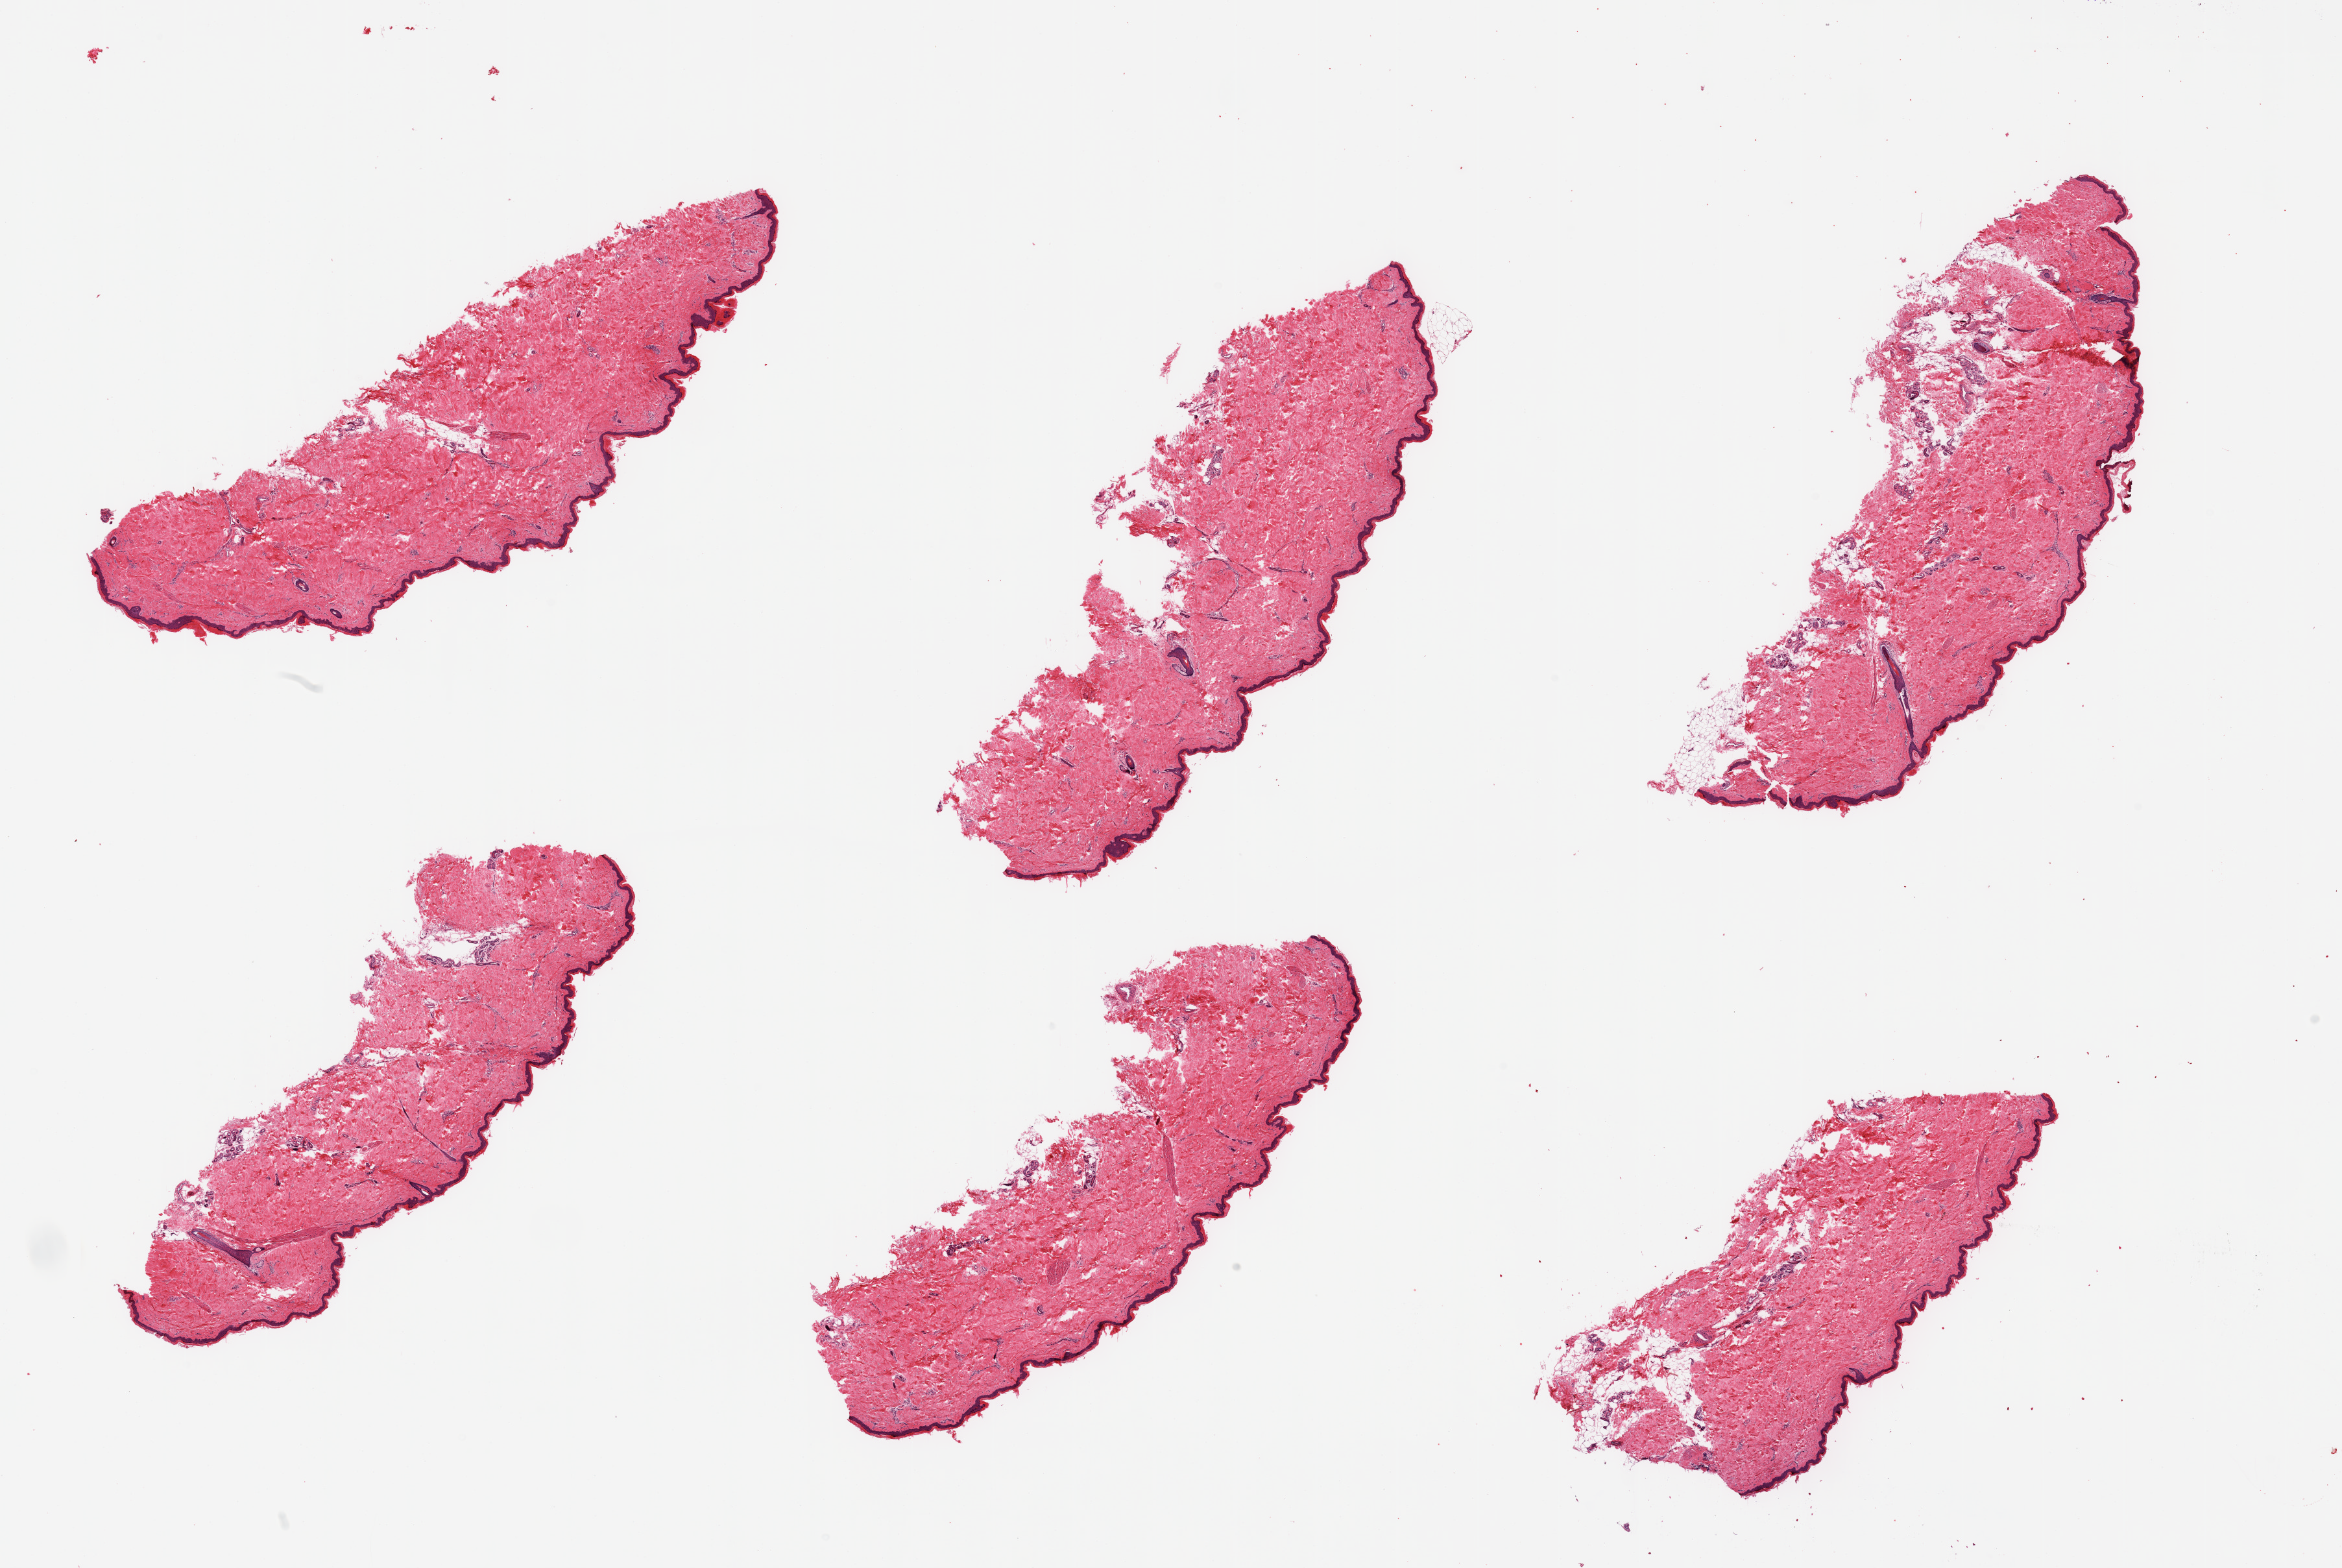
Hematoxylin and eosin (H&E) whole-slide image, brightfield — a low-resolution overview of the entire scanned area, about 28.5 x 19.1 mm, PAXgene-fixed, paraffin-embedded tissue, target tissue: skin of lower leg, donor tissue sample. Female donor.
Pathologist's review note for this sample: 6 pieces; well trimmed; 5% dermal fat.